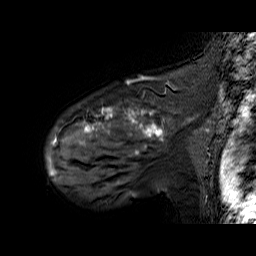
Breast MRI (dynamic contrast-enhanced), one sagittal slice; slice 49 of 60 in the series (ordered by position); dynamic contrast-enhanced series, time point 2 of 6 at this slice position (early post-contrast); 1.5 T; TE 6.3 ms, TR 32.9 ms; 4 mm slice thickness; 256 × 256 image matrix, field of view 200 × 200 mm. Female patient. Case-level facts recorded for this patient, not image findings: setting: breast cancer imaged before/during neoadjuvant chemotherapy; receptor status: HER2-positive.
Annotated regions visible in this slice (semi-automatic segmentation, software-assisted and operator-edited):
- analysis volume of interest (the breast-tissue region the enhancement analysis was run in; not a lesion): bounding box [x1, y1, x2, y2] px = [48, 92, 195, 174]
- tumour enhancement mask (voxels above the 100 % enhancement threshold inside the analysis volume of interest): [48, 107, 164, 174]